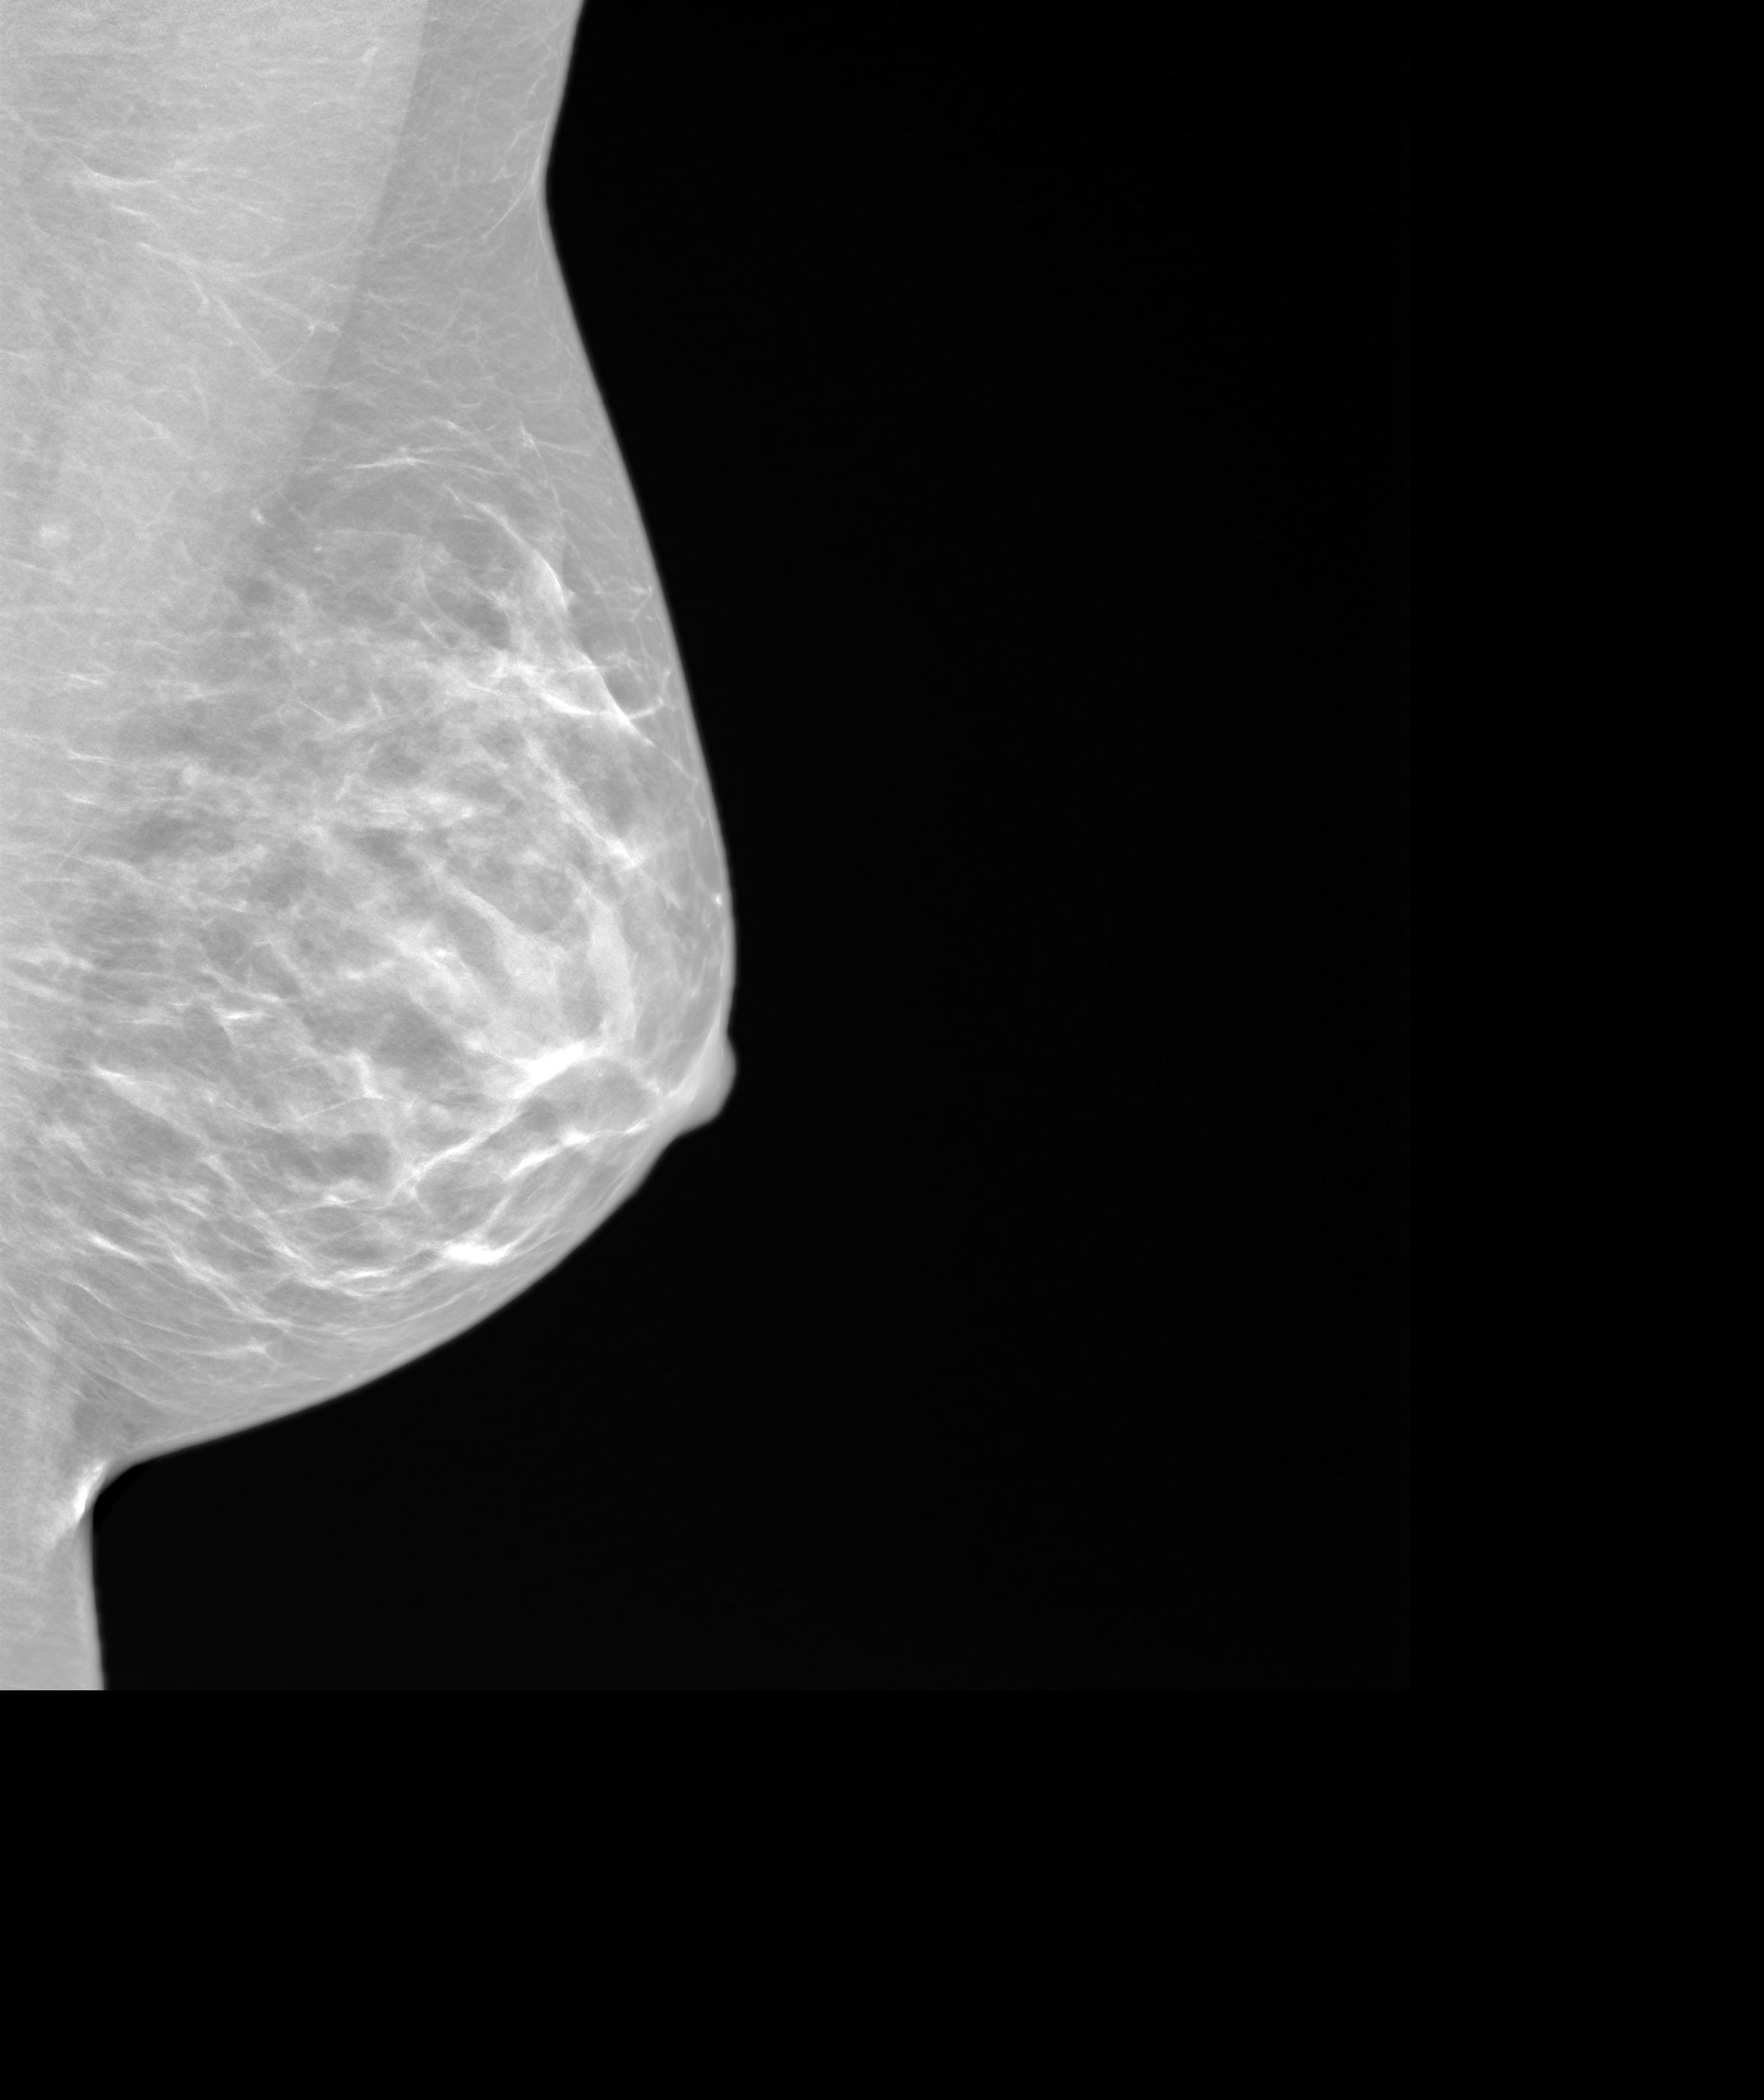
Screening examination; system: SenoIris_1SP2(440). Female patient, age 43 years.
Image type: synthesized 2-D view from tomosynthesis. Breast: left. Projection: medio-lateral oblique projection.